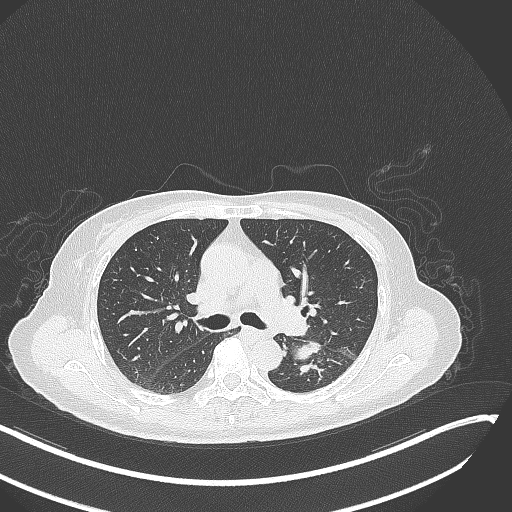
Chest CT, one axial slice; position 177 of 342 along the scan axis; reconstruction kernel B70f; lung window (W 1500 / L -600 HU); 1 mm slice thickness; 512 × 512 image matrix, field of view 400 × 400 mm. Female patient, age 64 years. Case-level facts recorded for this patient, not image findings: clinical TNM (as recorded): T3 N1 M1; histopathological grade: G3.
Structures marked on this image (bounding box drawn by a radiologist):
- lung tumour (recorded histology: small cell carcinoma): bounding box [x1, y1, x2, y2] px = [294, 339, 321, 361]